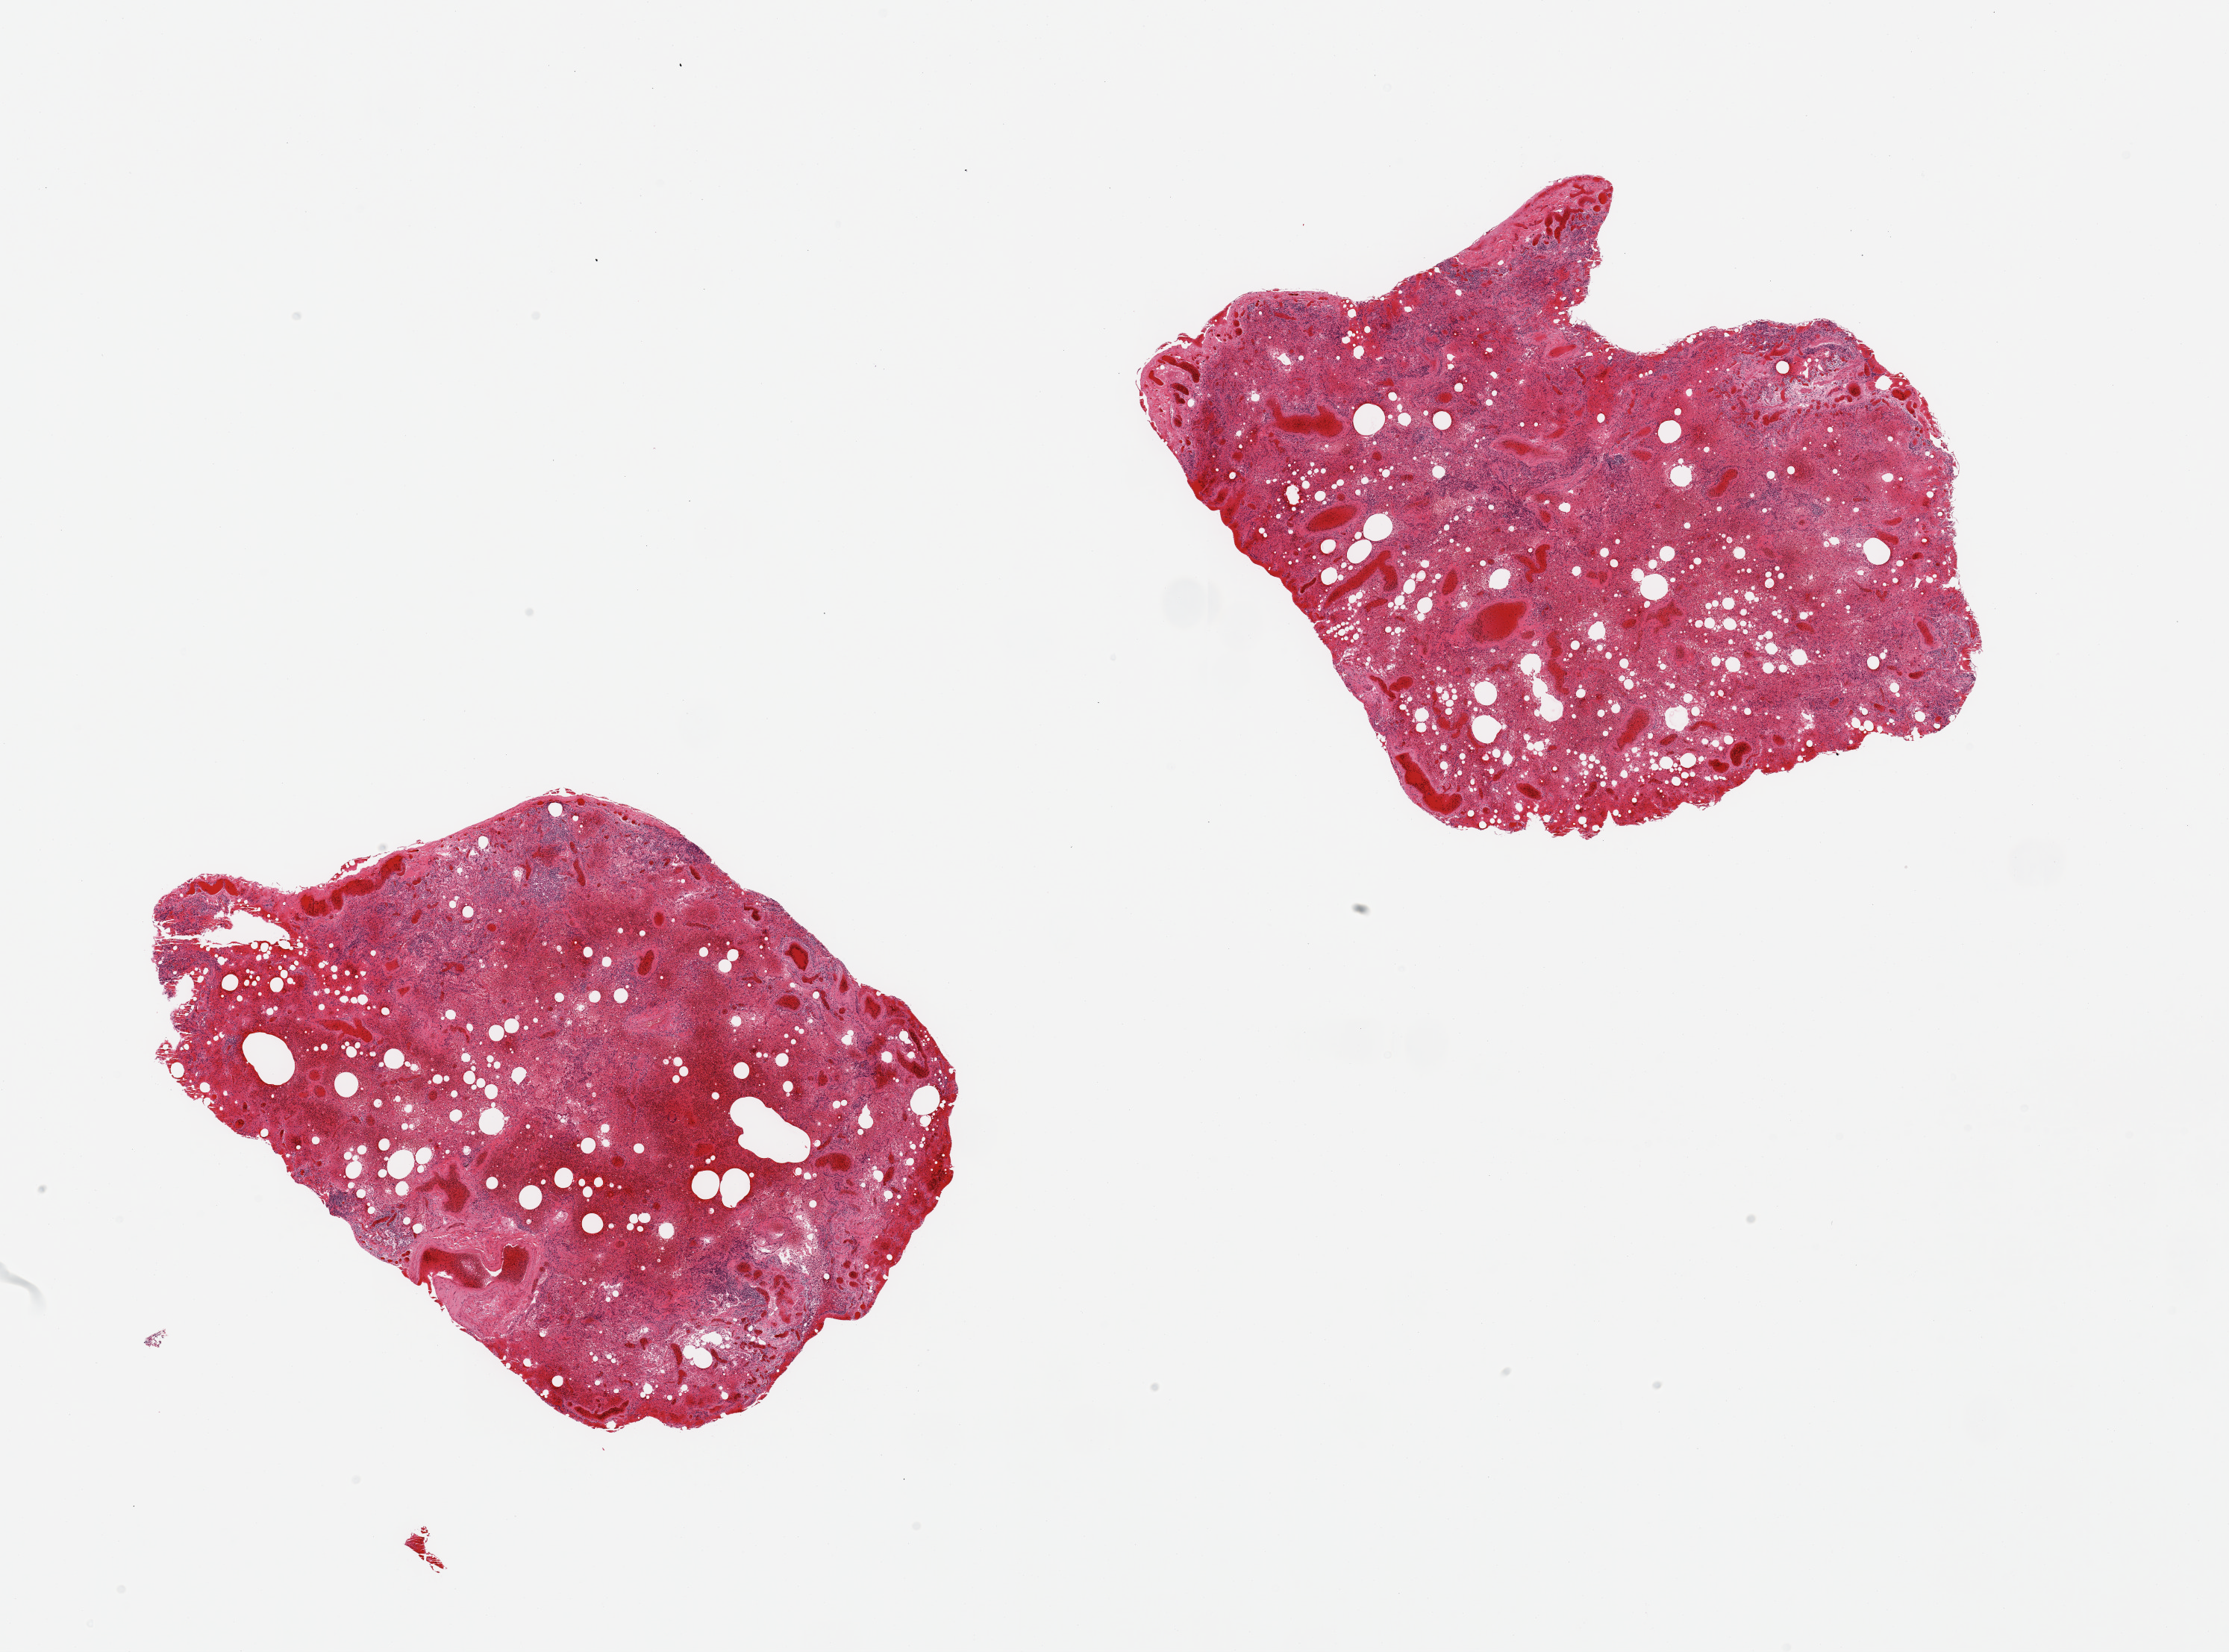
Whole-slide image, hematoxylin and eosin (H&E) stain, brightfield, whole scanned area (about 23.6 x 17.5 mm) shown as a low-resolution overview; PAXgene-fixed, paraffin-embedded tissue; sampled site (target tissue): lung; donor tissue sample.
• pathologist's review note for this sample: 2 pieces; extensive hemorrhage & congestion